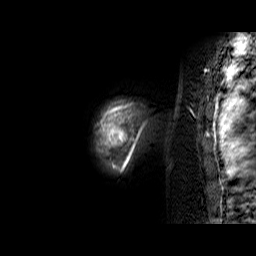
Breast MRI (dynamic contrast-enhanced), one sagittal slice; slice 57 of 60 in the series (ordered by position); dynamic contrast-enhanced series, time point 2 of 6 at this slice position (early post-contrast); 1.5 T; TE 6.4 ms, TR 32.9 ms; 4 mm slice thickness; 256 × 256 image matrix, field of view 200 × 200 mm. Female patient. From the clinical record (not read from this slice): setting: breast cancer imaged before/during neoadjuvant chemotherapy; receptor status: triple-negative.
Structures marked on this image (semi-automatic segmentation, software-assisted and operator-edited):
- analysis volume of interest (the breast-tissue region the enhancement analysis was run in; not a lesion): bounding box <97,102,148,174> (left, top, right, bottom; pixels)
- tumour enhancement mask (voxels above the 100 % enhancement threshold inside the analysis volume of interest): <97,102,147,173>